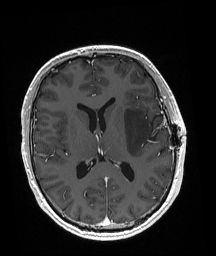
Brain MRI from a brain-tumour surgery series, one axial slice; position 91 of 192 along the scan axis; T1-weighted post-contrast; 1 mm slice thickness; 216 × 256 image matrix, field of view 211 × 250 mm. Case-level facts recorded for this patient, not image findings: histopathology: Astrocytoma; WHO grade: 3; IDH mutation: yes; tumour location: Left Posterior Frontal.
Annotated regions visible in this slice (outlined manually by an expert reader):
- tumour: bounding box [x1, y1, x2, y2] px = [124, 109, 152, 157]